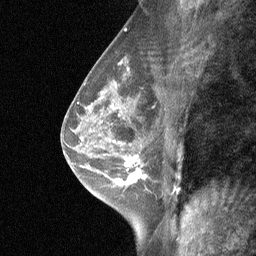
Breast MRI (dynamic contrast-enhanced), one sagittal slice. Position 36 of 64 along the scan axis. Dynamic contrast-enhanced study with each time point stored as its own series, time point 2 of 3 at this slice position (early post-contrast, ordered by acquisition time). 1.5 T. TE 4.8 ms, TR 27 ms. 2 mm slice thickness. 256 × 256 image matrix. Patient: female, 47 years. From the clinical record (not read from this slice): setting: breast cancer imaged before/during neoadjuvant chemotherapy; receptor status: HR-positive, HER2-negative.
Annotated regions visible in this slice (semi-automatically segmented with operator editing):
- analysis volume of interest (the breast-tissue region the enhancement analysis was run in; not a lesion): bounding box <104,138,165,198> (left, top, right, bottom; pixels)
- tumour enhancement mask (voxels above the 90 % enhancement threshold inside the analysis volume of interest): <116,156,145,186>